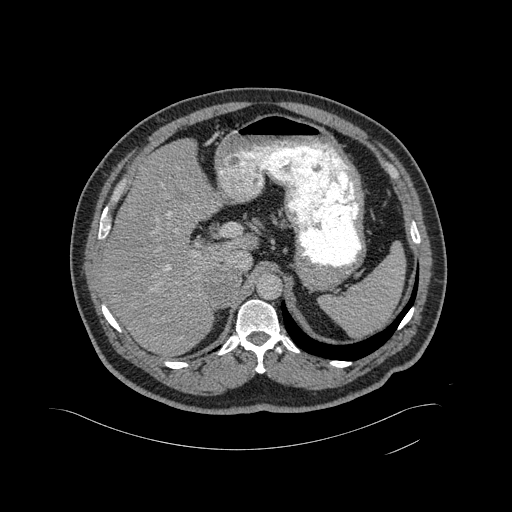
Contrast-enhanced abdominal CT, one axial slice; slice 332 of 433 in the series (ordered by position); 120 kVp; intravenous contrast given; soft-tissue window (W 400 / L 40 HU); 2 mm slice thickness; 512 × 512 image matrix, field of view 500 × 500 mm. Patient: male, 56 years. Case-level facts recorded for this patient, not image findings: diagnosis: adrenocortical carcinoma; tumour side: right adrenal; tumour size at pathology: 11.6 cm; Ki-67 index: 50 %; stage (as recorded): 3.
Outlined on this slice (semi-automatically segmented with operator editing):
- mass: bounding box (x1, y1, x2, y2) in pixels: (204, 270, 240, 305)